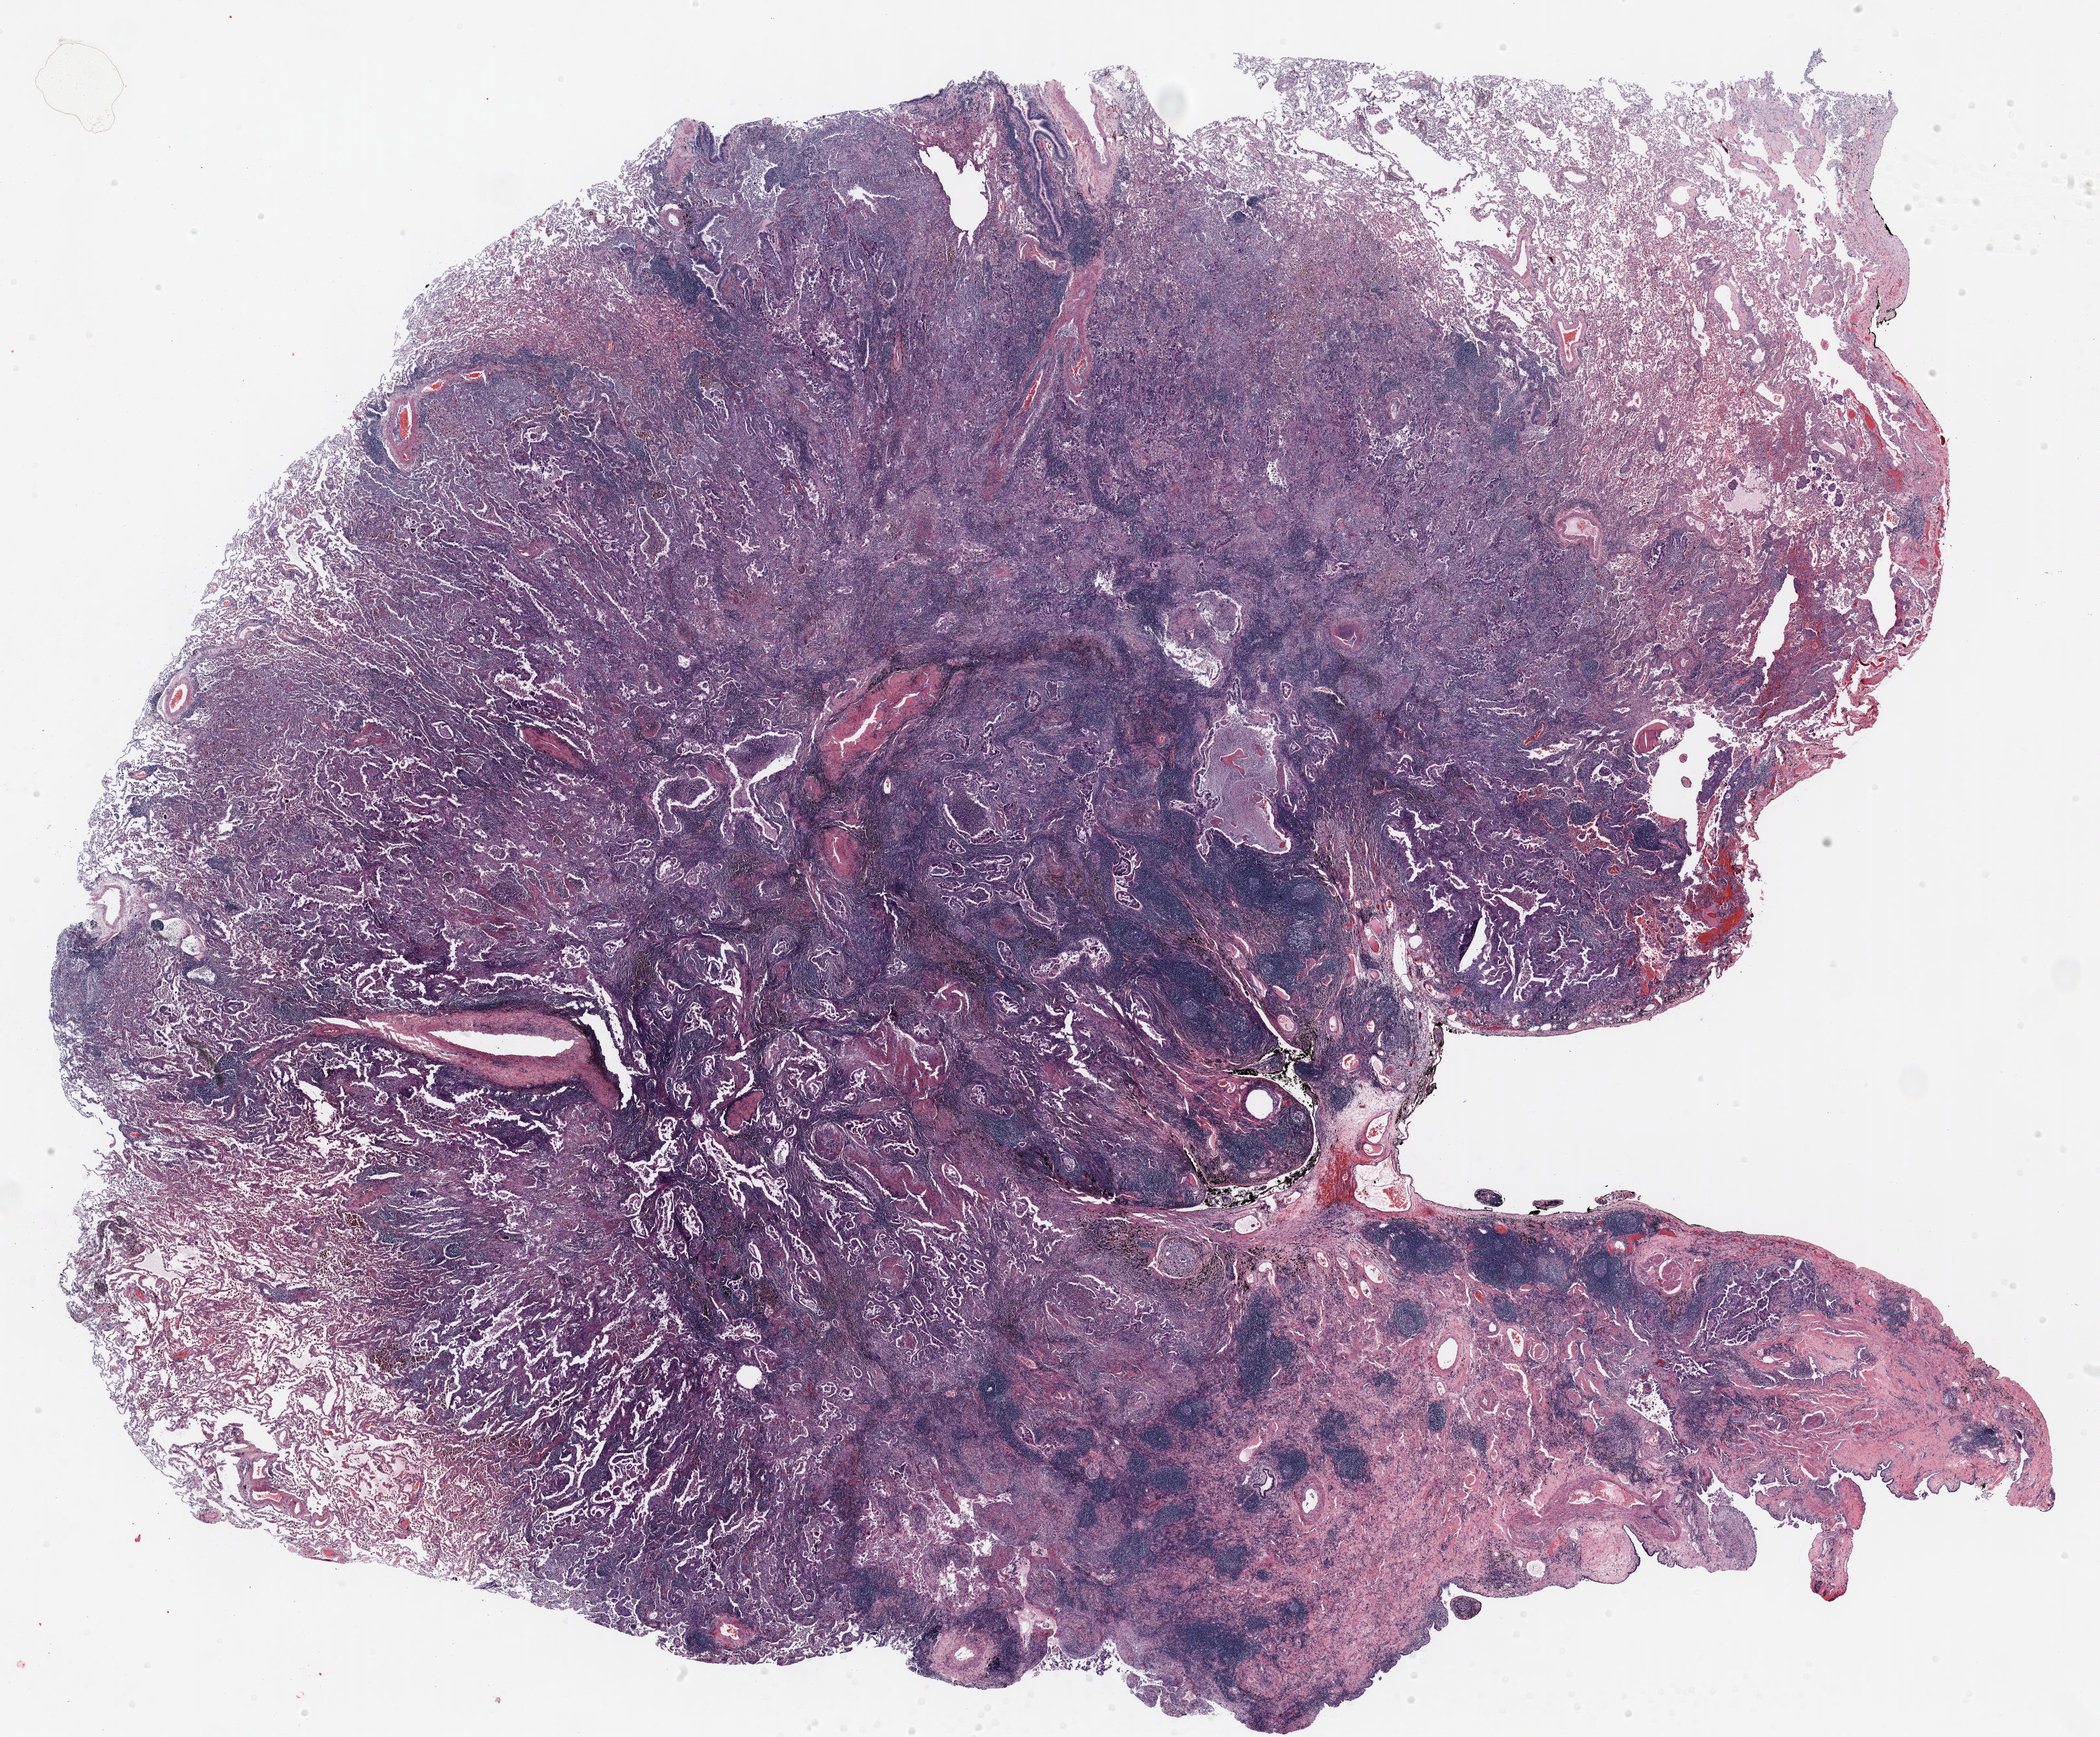
H&E-stained whole-slide image — whole scanned area (about 26.0 x 21.5 mm, from a 20x scan) shown as a low-resolution overview. FFPE section. Lung. Male patient, aged 66 at enrolment. Current smoker at enrolment.
Participant's lung-cancer diagnosis: Squamous cell carcinoma, adenoid.